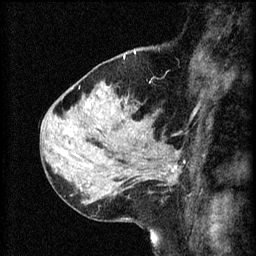
Breast MRI (dynamic contrast-enhanced), one sagittal slice; 3 images stored at this slice position (order not interpretable as contrast timing); 1.5 T; TE 4.2 ms, TR 8.2 ms; 2 mm slice thickness; 256 × 256 image matrix, field of view 180 × 180 mm. Female patient, age 37 years.
Structures marked on this image (semi-automatically segmented with operator editing):
- analysis volume of interest (the breast-tissue region the enhancement analysis was run in; not a lesion): bounding box (x1, y1, x2, y2) in pixels: (124, 138, 185, 193)
- tumour enhancement mask (voxels above the 70 % enhancement threshold inside the analysis volume of interest): (147, 152, 178, 181)